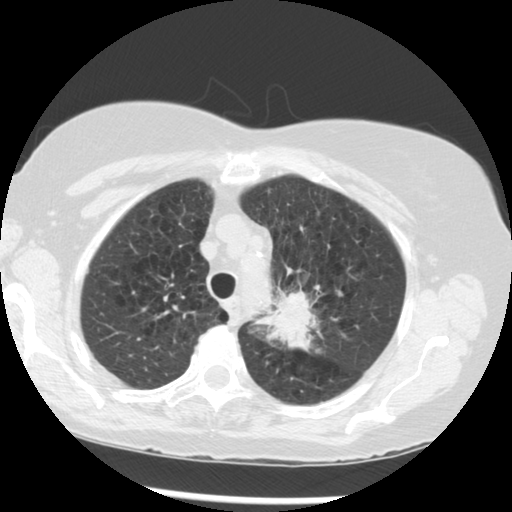
Chest CT (low-dose screening protocol), one axial image, third annual screen, lung window (W 1500 / L -600 HU), 2.5 mm slice thickness, 120 kVp, slice 222 of 283 in the series. Female, age 70 years at enrolment. Current smoker at enrolment.
- Expert-annotated lung lesion, bounding box <261,273,356,362> (left, top, right, bottom; pixels).
- The exam's reader record, not a measurement of the box and not confirmed to be the same lesion: non-calcified nodule or mass ≥4 mm, left upper lobe, 32 × 26 mm, spiculated (stellate) margins, soft tissue attenuation, pre-existing on the prior screen: yes; interval growth: yes.
- Official screen result: positive, other.
- Later outcome: lung cancer diagnosed 24 days after this screen — neoplasm, malignant, left upper lobe, stage IIIB (AJCC 6th edition), 40 mm at pathology.